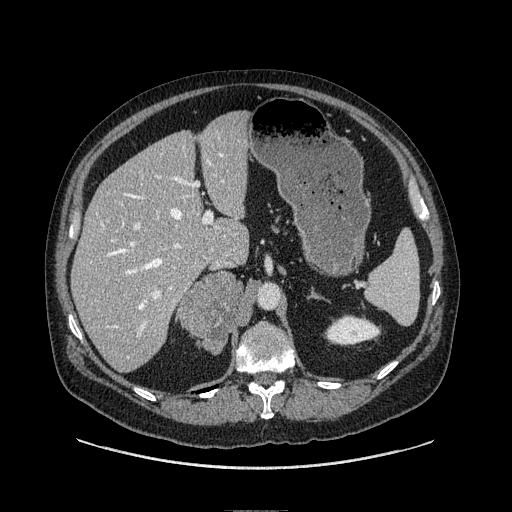
Contrast-enhanced abdominal CT, one axial slice; position 60 of 149 along the scan axis; soft-tissue window (W 400 / L 40 HU); 512 × 512 image matrix, field of view 440 × 440 mm. Male patient. Case-level facts recorded for this patient, not image findings: diagnosis: adrenocortical carcinoma; tumour side: right adrenal; tumour size at pathology: 7.5 cm; Ki-67 index: 15 %; stage (as recorded): 2.
Annotated regions visible in this slice (semi-automatic segmentation, software-assisted and operator-edited):
- mass: bounding box (x1, y1, x2, y2) in pixels: (180, 274, 244, 353)